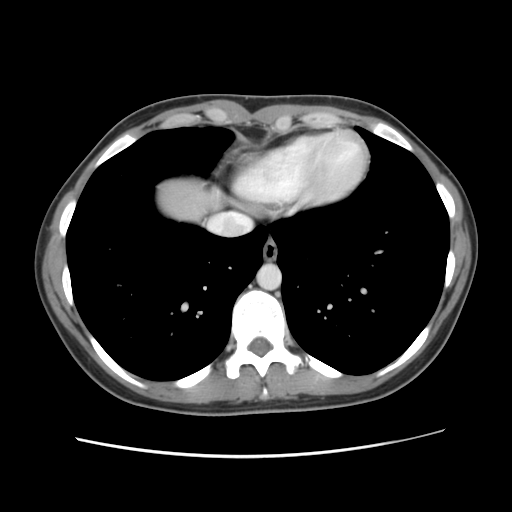
Contrast-enhanced abdominal CT, one axial slice. Position 119 of 134 along the scan axis. Intravenous contrast given. Soft-tissue window (W 400 / L 40 HU). 2.5 mm slice thickness. 512 × 512 image matrix. Female patient, age 33 years. From the clinical record (not read from this slice): diagnosis: colorectal cancer liver metastases, imaged before liver resection; multiple liver metastases: yes; largest metastasis: 4.5 cm; disease in both lobes: yes.
Annotated regions visible in this slice (expert manual segmentation):
- liver: bounding box [x1, y1, x2, y2] px = [157, 177, 223, 223]
- planned liver remnant (the part of the liver to remain after resection): [158, 177, 222, 223]